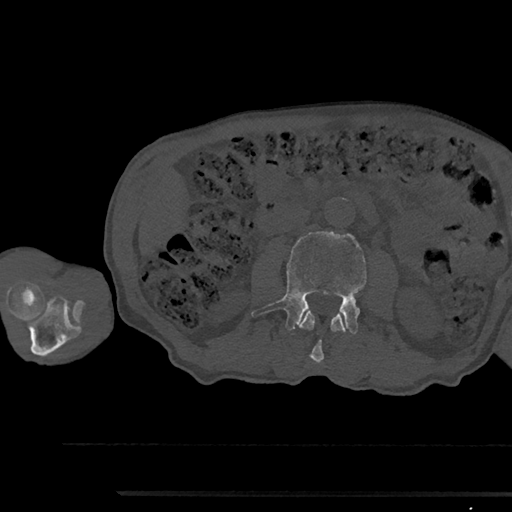
CT including the spine, one axial slice; position 516 of 797 along the scan axis; 120 kVp; bone window (W 1800 / L 400 HU); 0.5 mm slice thickness; 512 × 512 image matrix, field of view 367 × 367 mm. Patient: male, 79 years. From the clinical record (not read from this slice): primary cancer: prostate.
Outlined on this slice (semi-automatically segmented with operator editing):
- L2 vertebra: bounding box (x1, y1, x2, y2) in pixels: (298, 310, 347, 363)
- L3 vertebra: (251, 231, 366, 334)